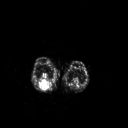
FDG PET of an extremity soft-tissue mass (from a PET/CT study), one axial slice. Slice 165 of 267 in the series (ordered by position). 3.27 mm slice thickness. 128 × 128 image matrix. Patient: female, 62 years. Case-level facts recorded for this patient, not image findings: histological type: liposarcoma; site of the primary tumour: right thigh.
Structures marked on this image (expert contour drawn on MRI and transferred to this co-registered scan by the dataset authors):
- gross tumour volume (mass): box from (x=39, y=78) to (x=50, y=90) px